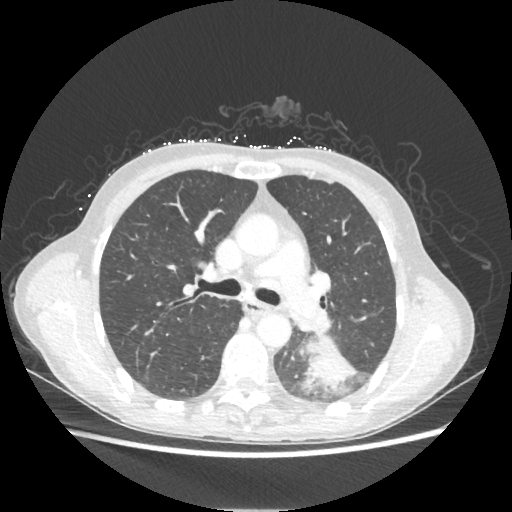
Chest CT, one axial slice. Position 137 of 221 along the scan axis. Lung window (W 1500 / L -600 HU). 512 × 512 image matrix, field of view 360 × 360 mm. Patient: female, 53 years. From the clinical record (not read from this slice): clinical TNM (as recorded): T3 N0 M0.
Annotated regions visible in this slice (bounding box drawn by a radiologist):
- lung tumour (recorded histology: adenocarcinoma): box from (x=303, y=337) to (x=355, y=389) px